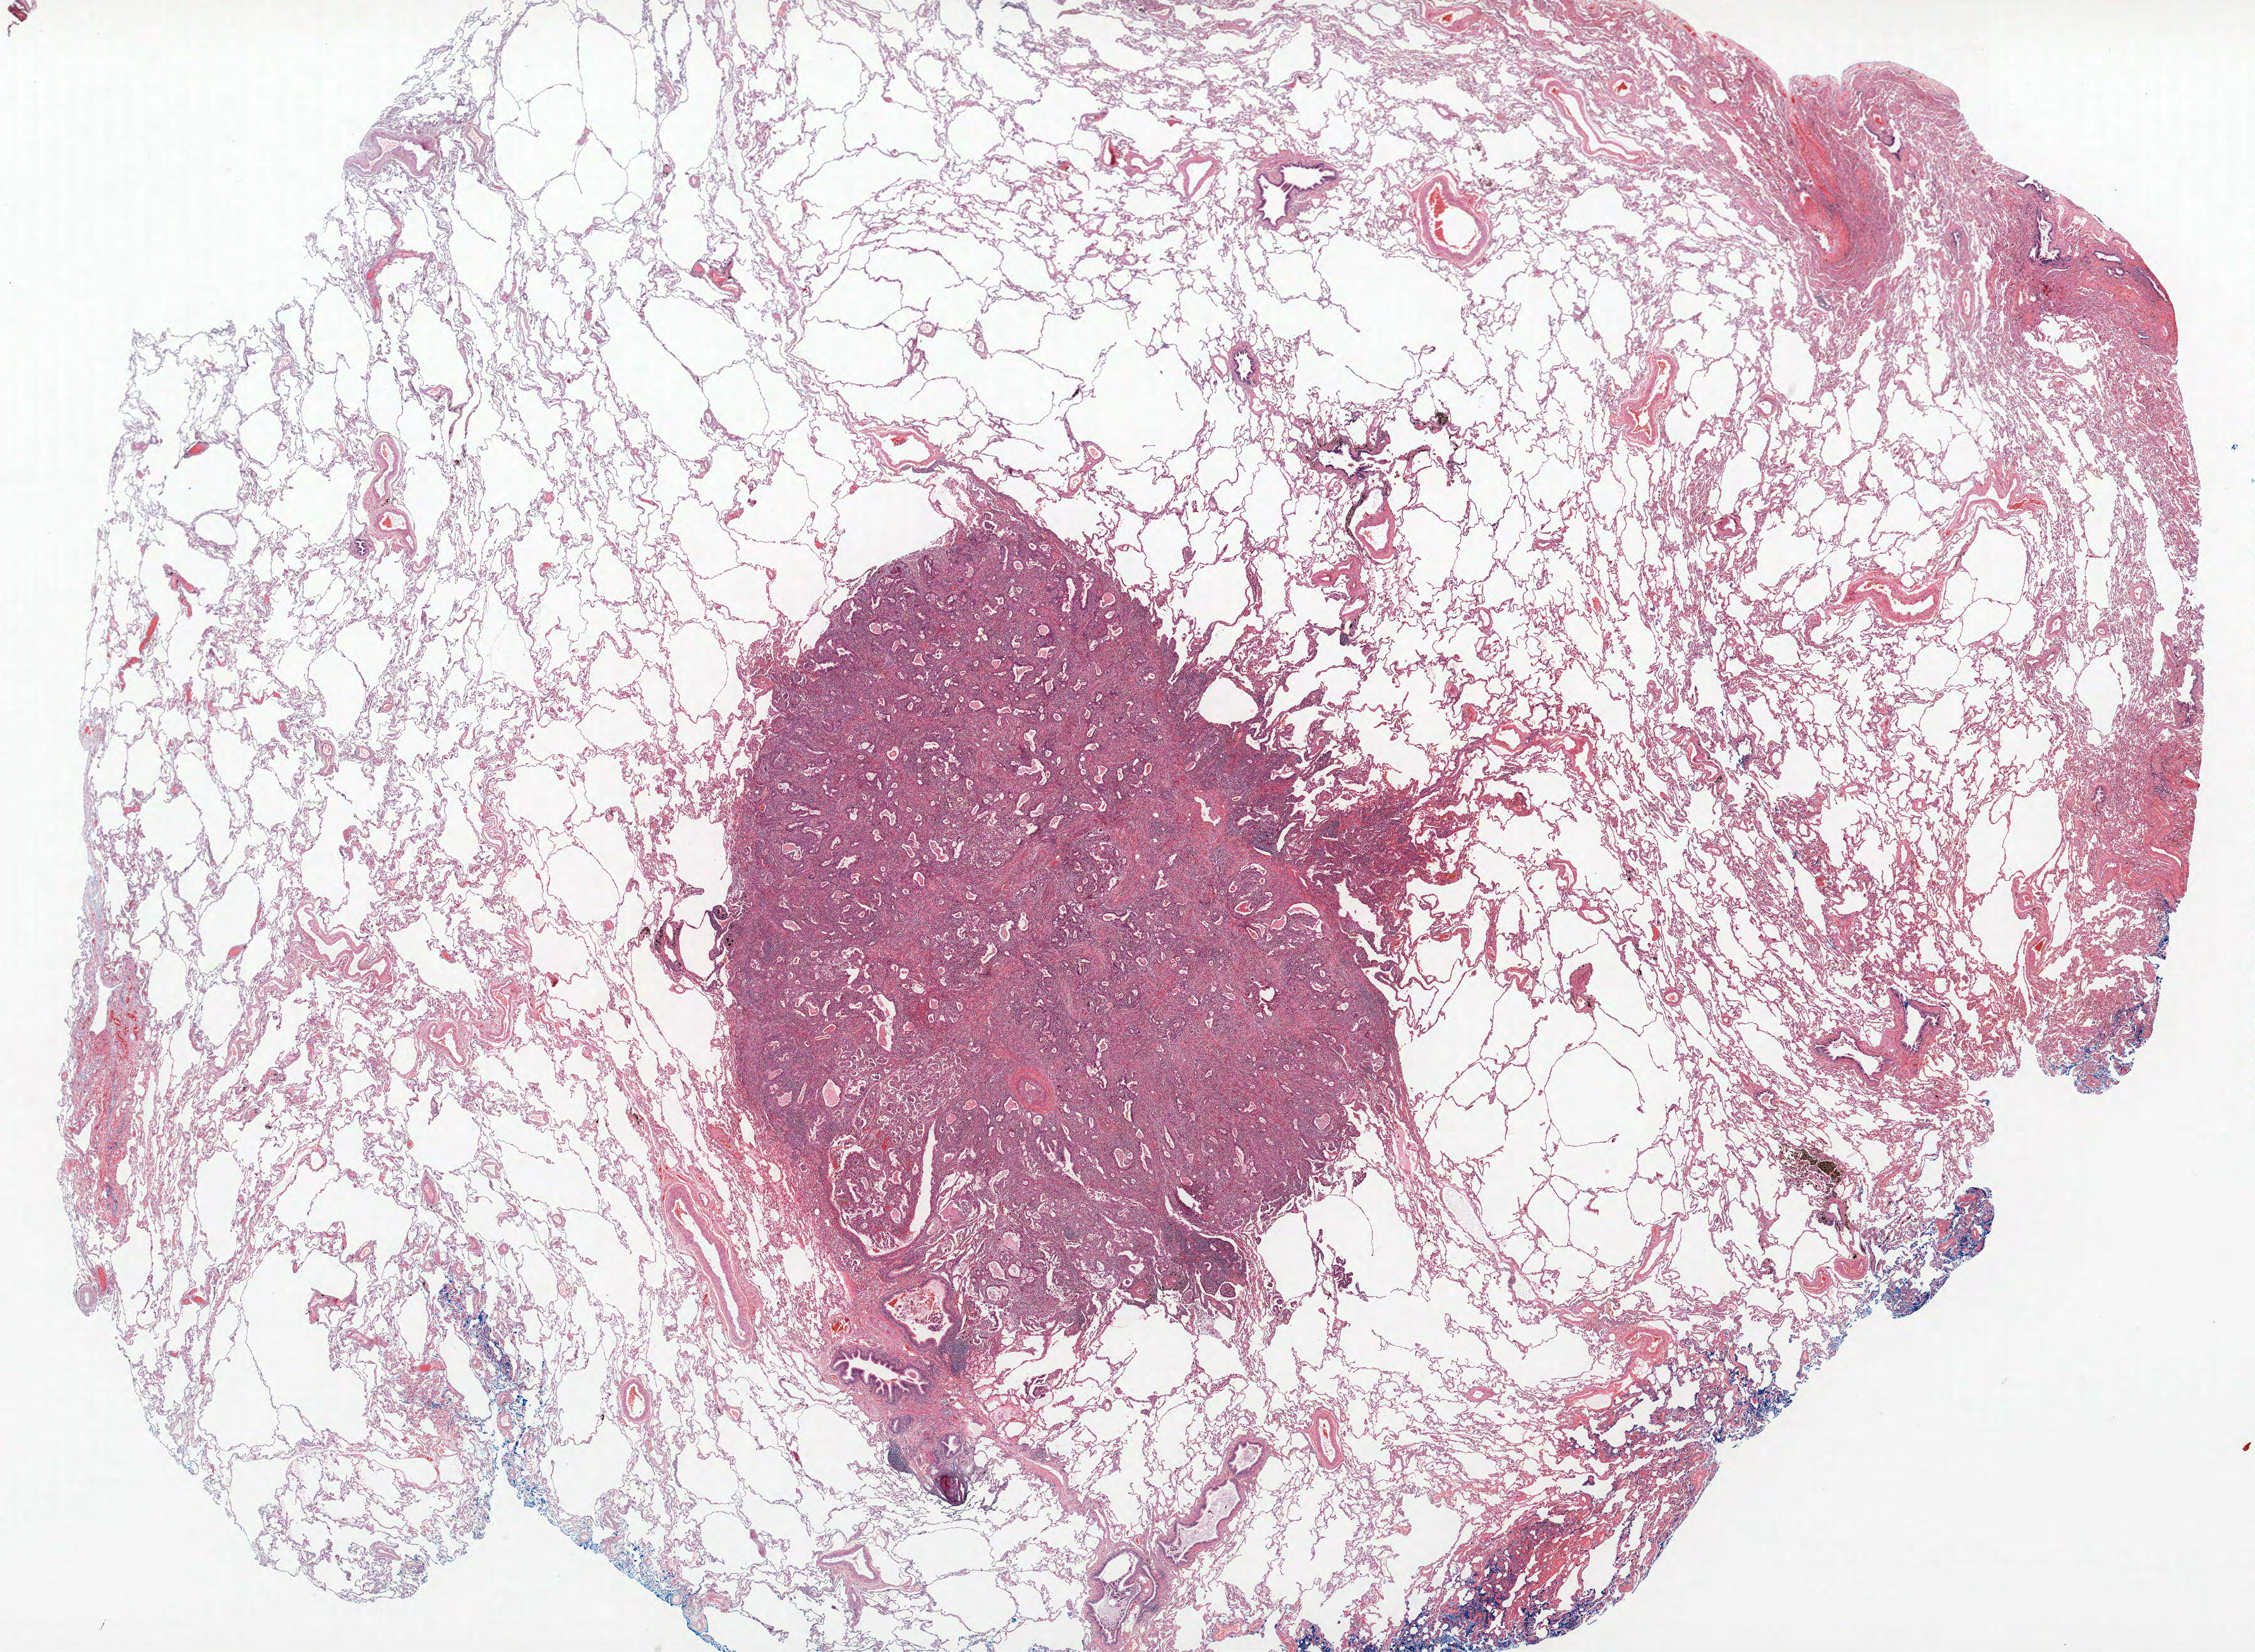
H&E whole-slide image, low-resolution overview of the scanned area, about 28.6 x 20.9 mm (slide scanned at 40x); formalin-fixed paraffin-embedded (FFPE) section; lung. Male, age 61 at enrolment. Former smoker at enrolment. Grade: moderately differentiated (G2).
* tumour size (pathology): 30 mm
* participant's lung-cancer diagnosis: Adenocarcinoma, NOS (ICD-O-3 8140/3)
* stage (AJCC 6th edition): IA
* primary tumour location (clinical record): right lower lobe